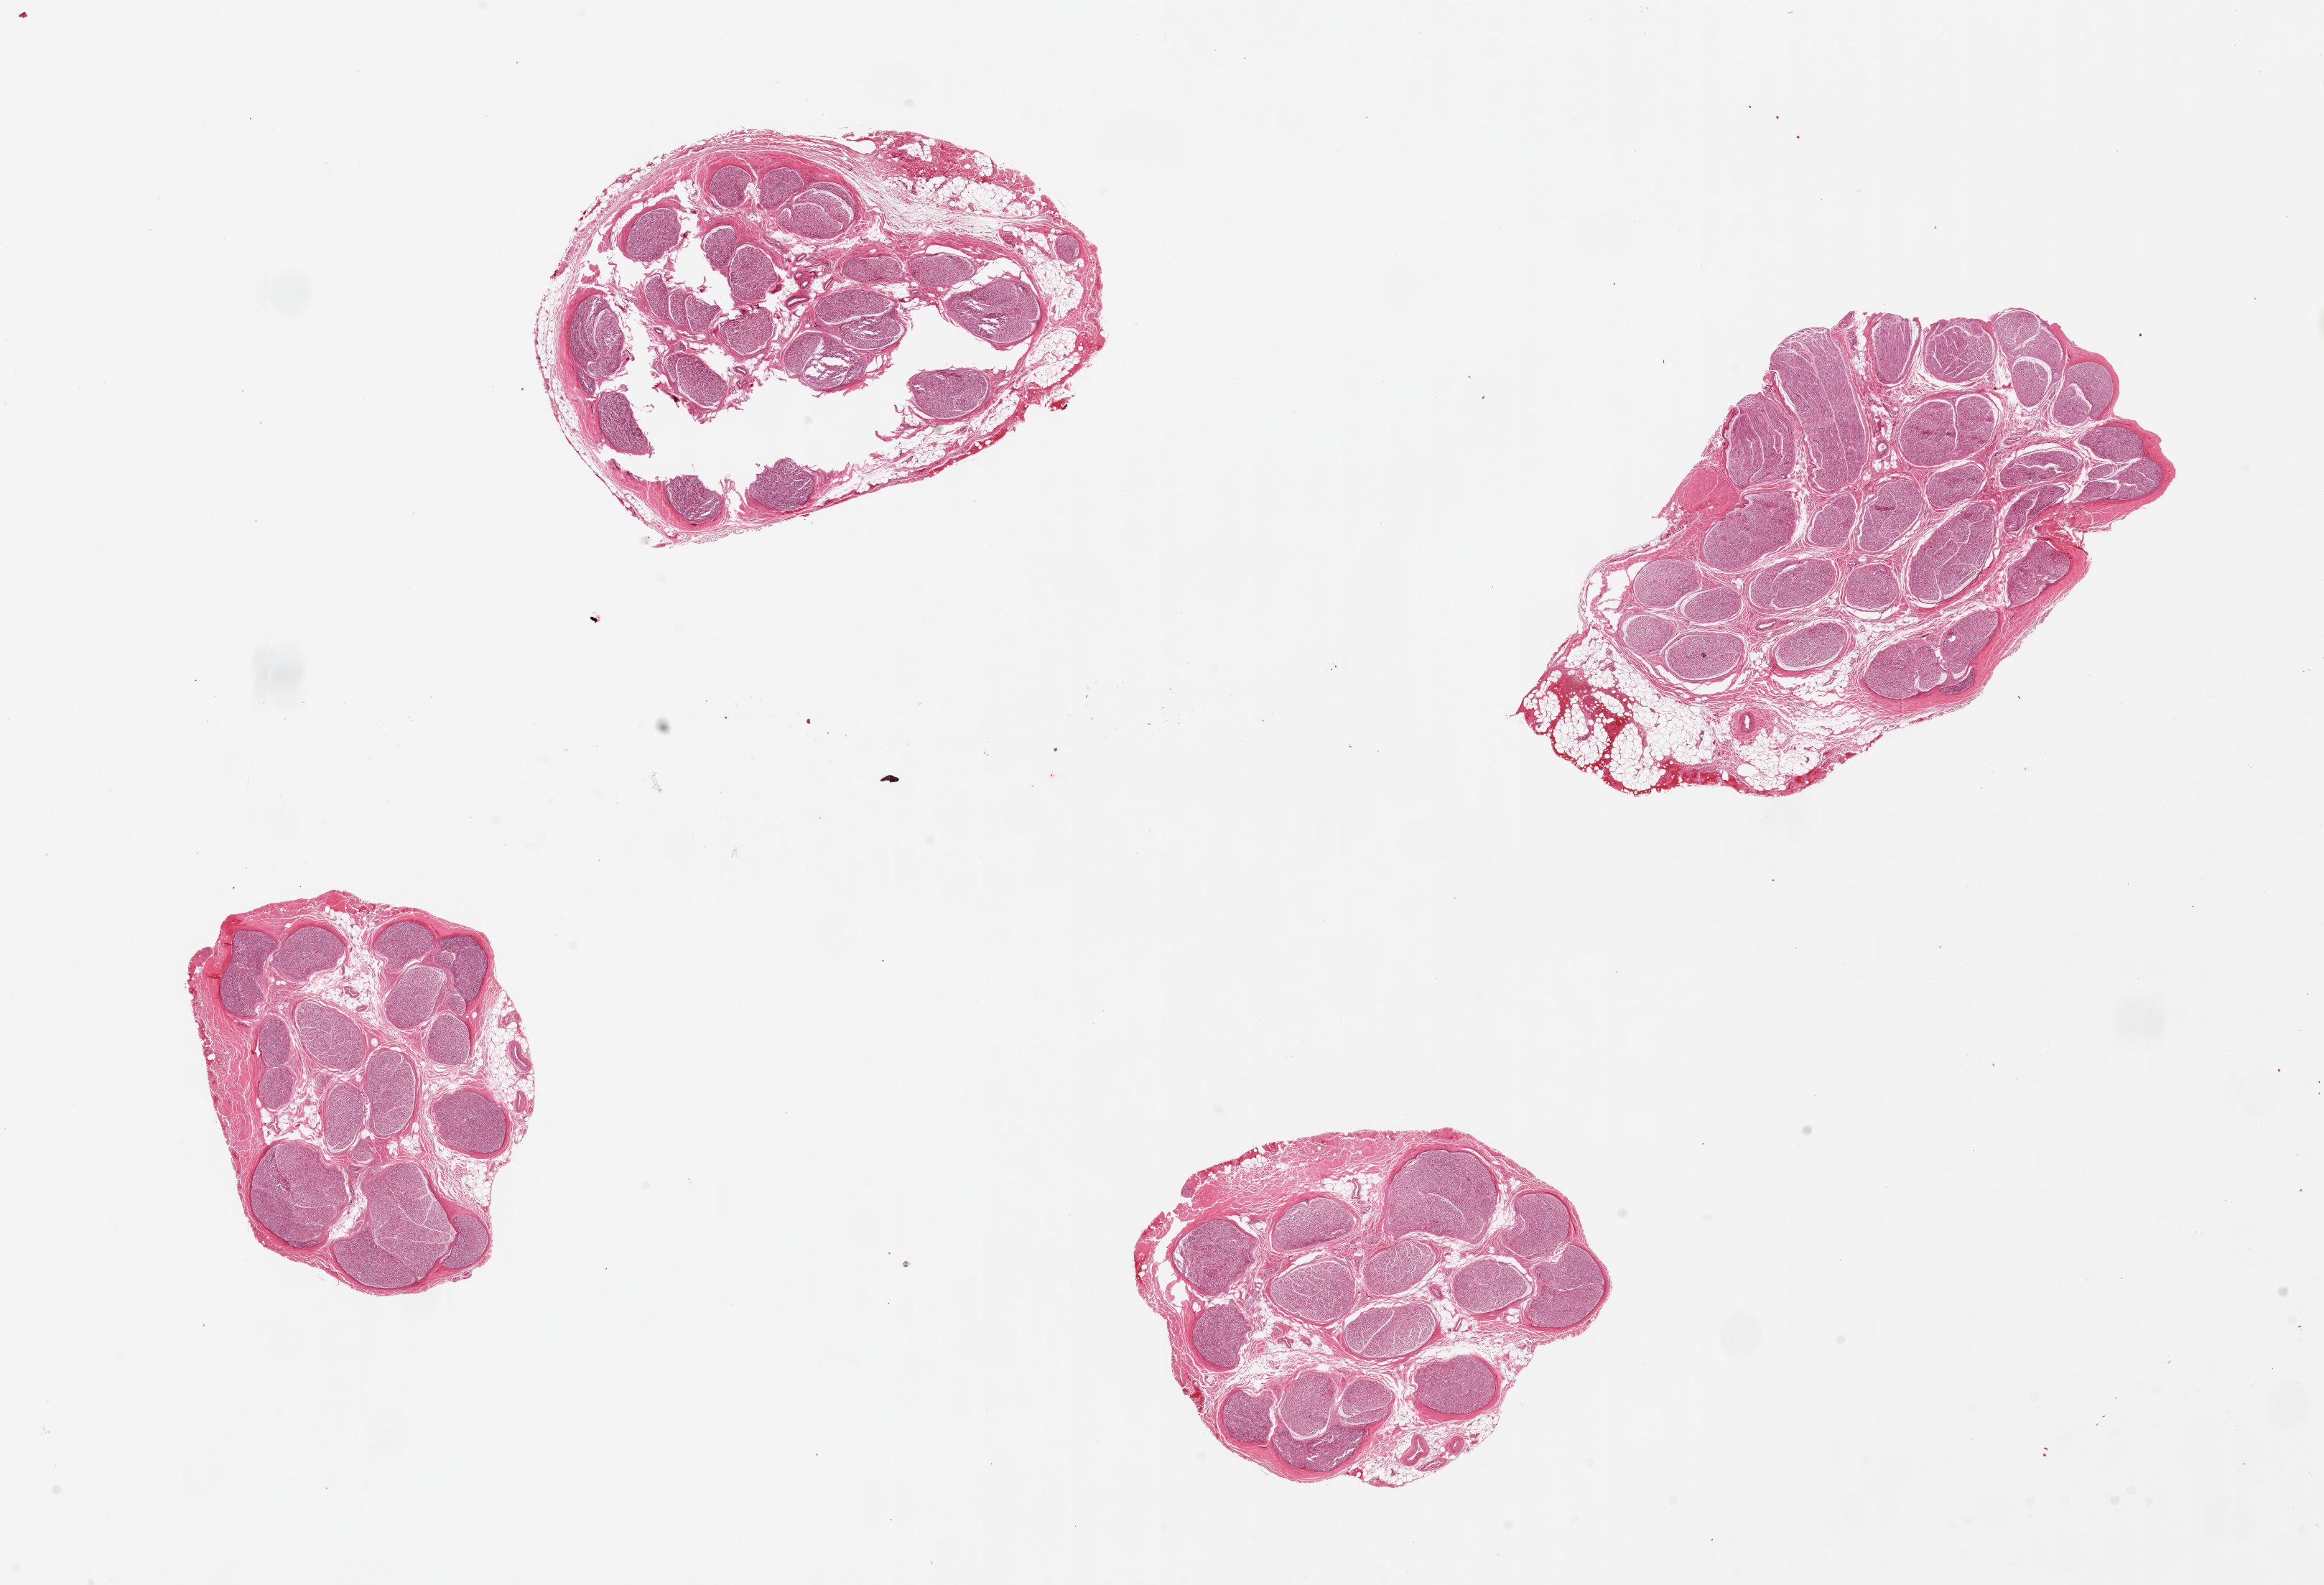
Whole-slide image, H&E stain, low-resolution overview of the scanned area, about 25.6 x 17.5 mm (from a 20x scan); PAXgene-fixed paraffin-embedded (PFPE) section; sampled site (target tissue): tibial nerve; donor tissue sample. Male donor.
Pathologist's review note for this sample: 2 pieces, not artery as originally labeled; nerve with some internal and up to 1.3mm attached adipose tissue.